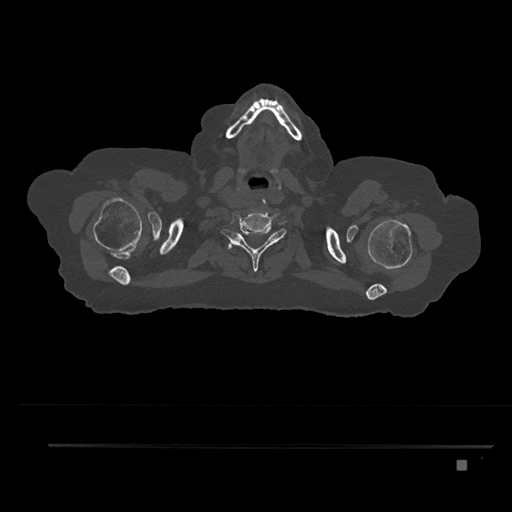
CT including the spine, one axial slice. Position 729 of 797 along the scan axis. Reconstruction kernel Br40s/3. Bone window (W 1800 / L 400 HU). 0.5 mm slice thickness. 512 × 512 image matrix. Female patient, age 76 years. Case-level facts recorded for this patient, not image findings: primary cancer: lung.
Annotated regions visible in this slice (semi-automatically segmented with operator editing):
- T1 vertebra: bounding box (x1, y1, x2, y2) in pixels: (229, 240, 250, 254)